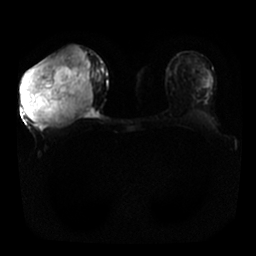
Breast MRI, one axial slice; slice 12 of 25 in the series (ordered by position); diffusion-weighted series; image 2 of 4 stored at this slice position (different b-values; order by instance number); 1.5 T; 4 mm slice thickness; 256 × 256 image matrix, field of view 340 × 340 mm. Female patient.
Annotated regions visible in this slice (manually delineated by an expert):
- tumour on diffusion-weighted imaging: box from (x=20, y=44) to (x=93, y=125) px